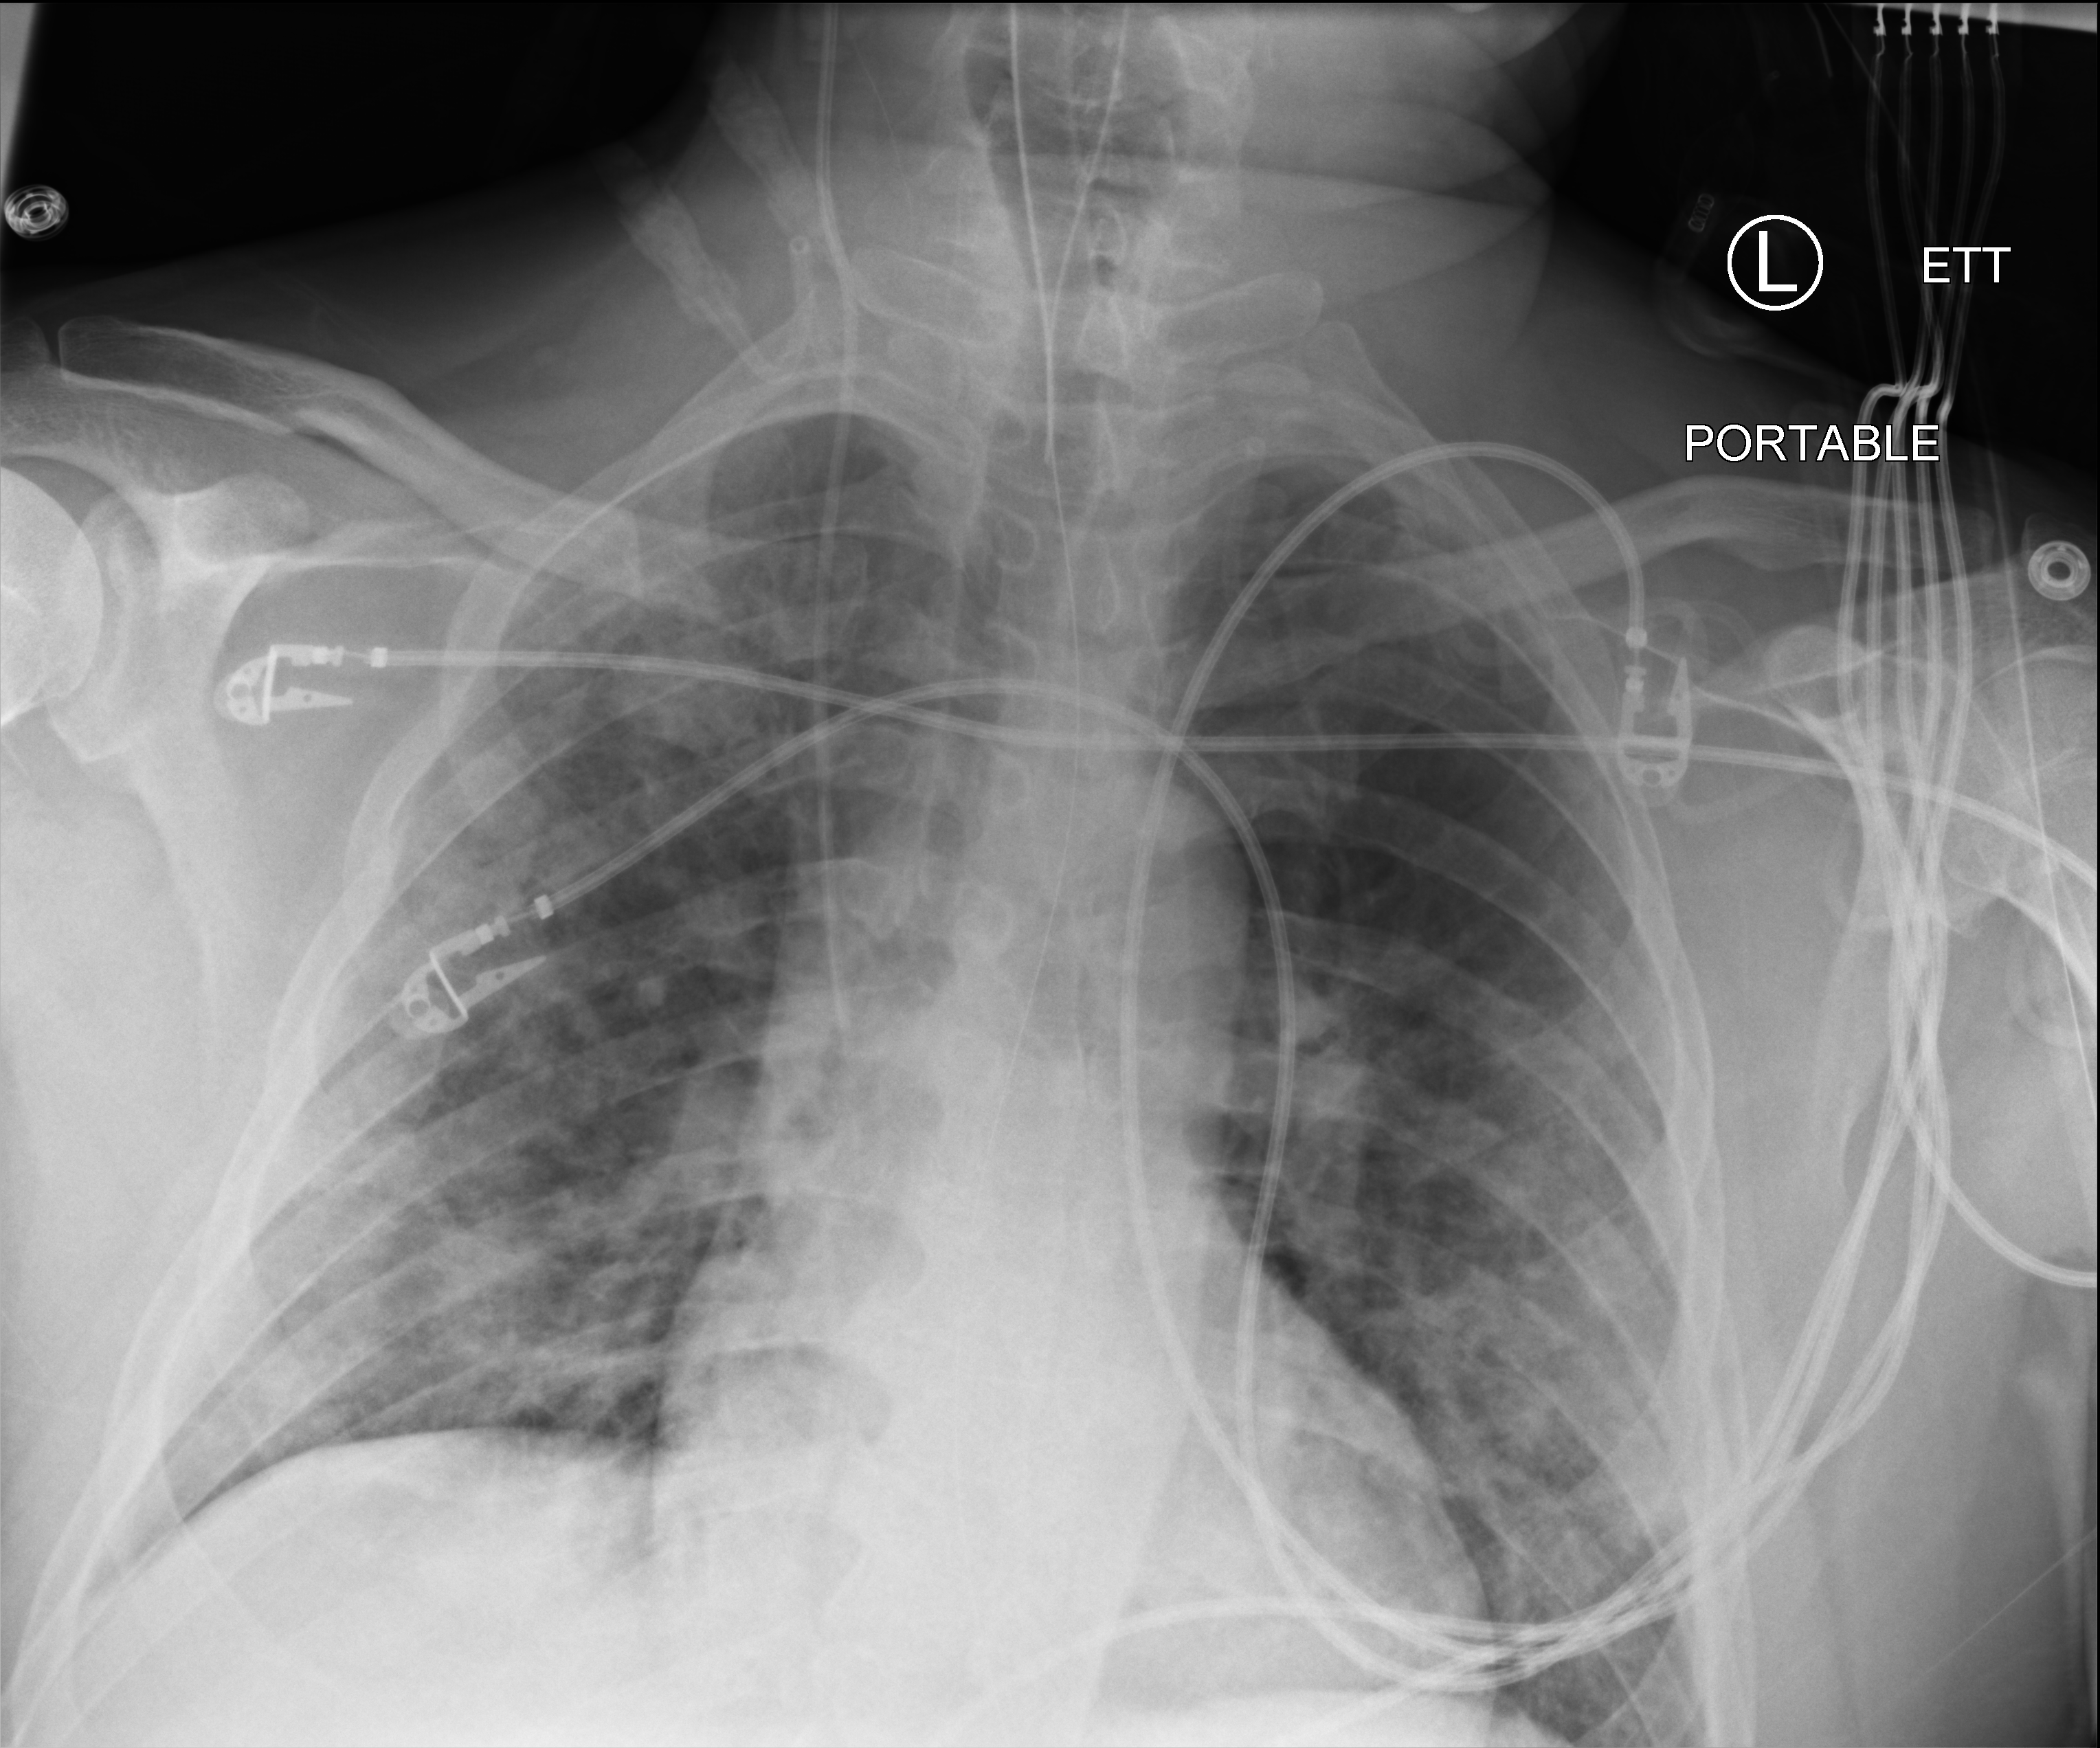
Chest X-ray (portable); anteroposterior (AP) projection. Patient hospitalised with COVID-19; male, aged 18–59 years.
Admission-level facts for this patient (not findings on this image; timing relative to this image not recorded): mechanically ventilated during this hospital stay: yes.